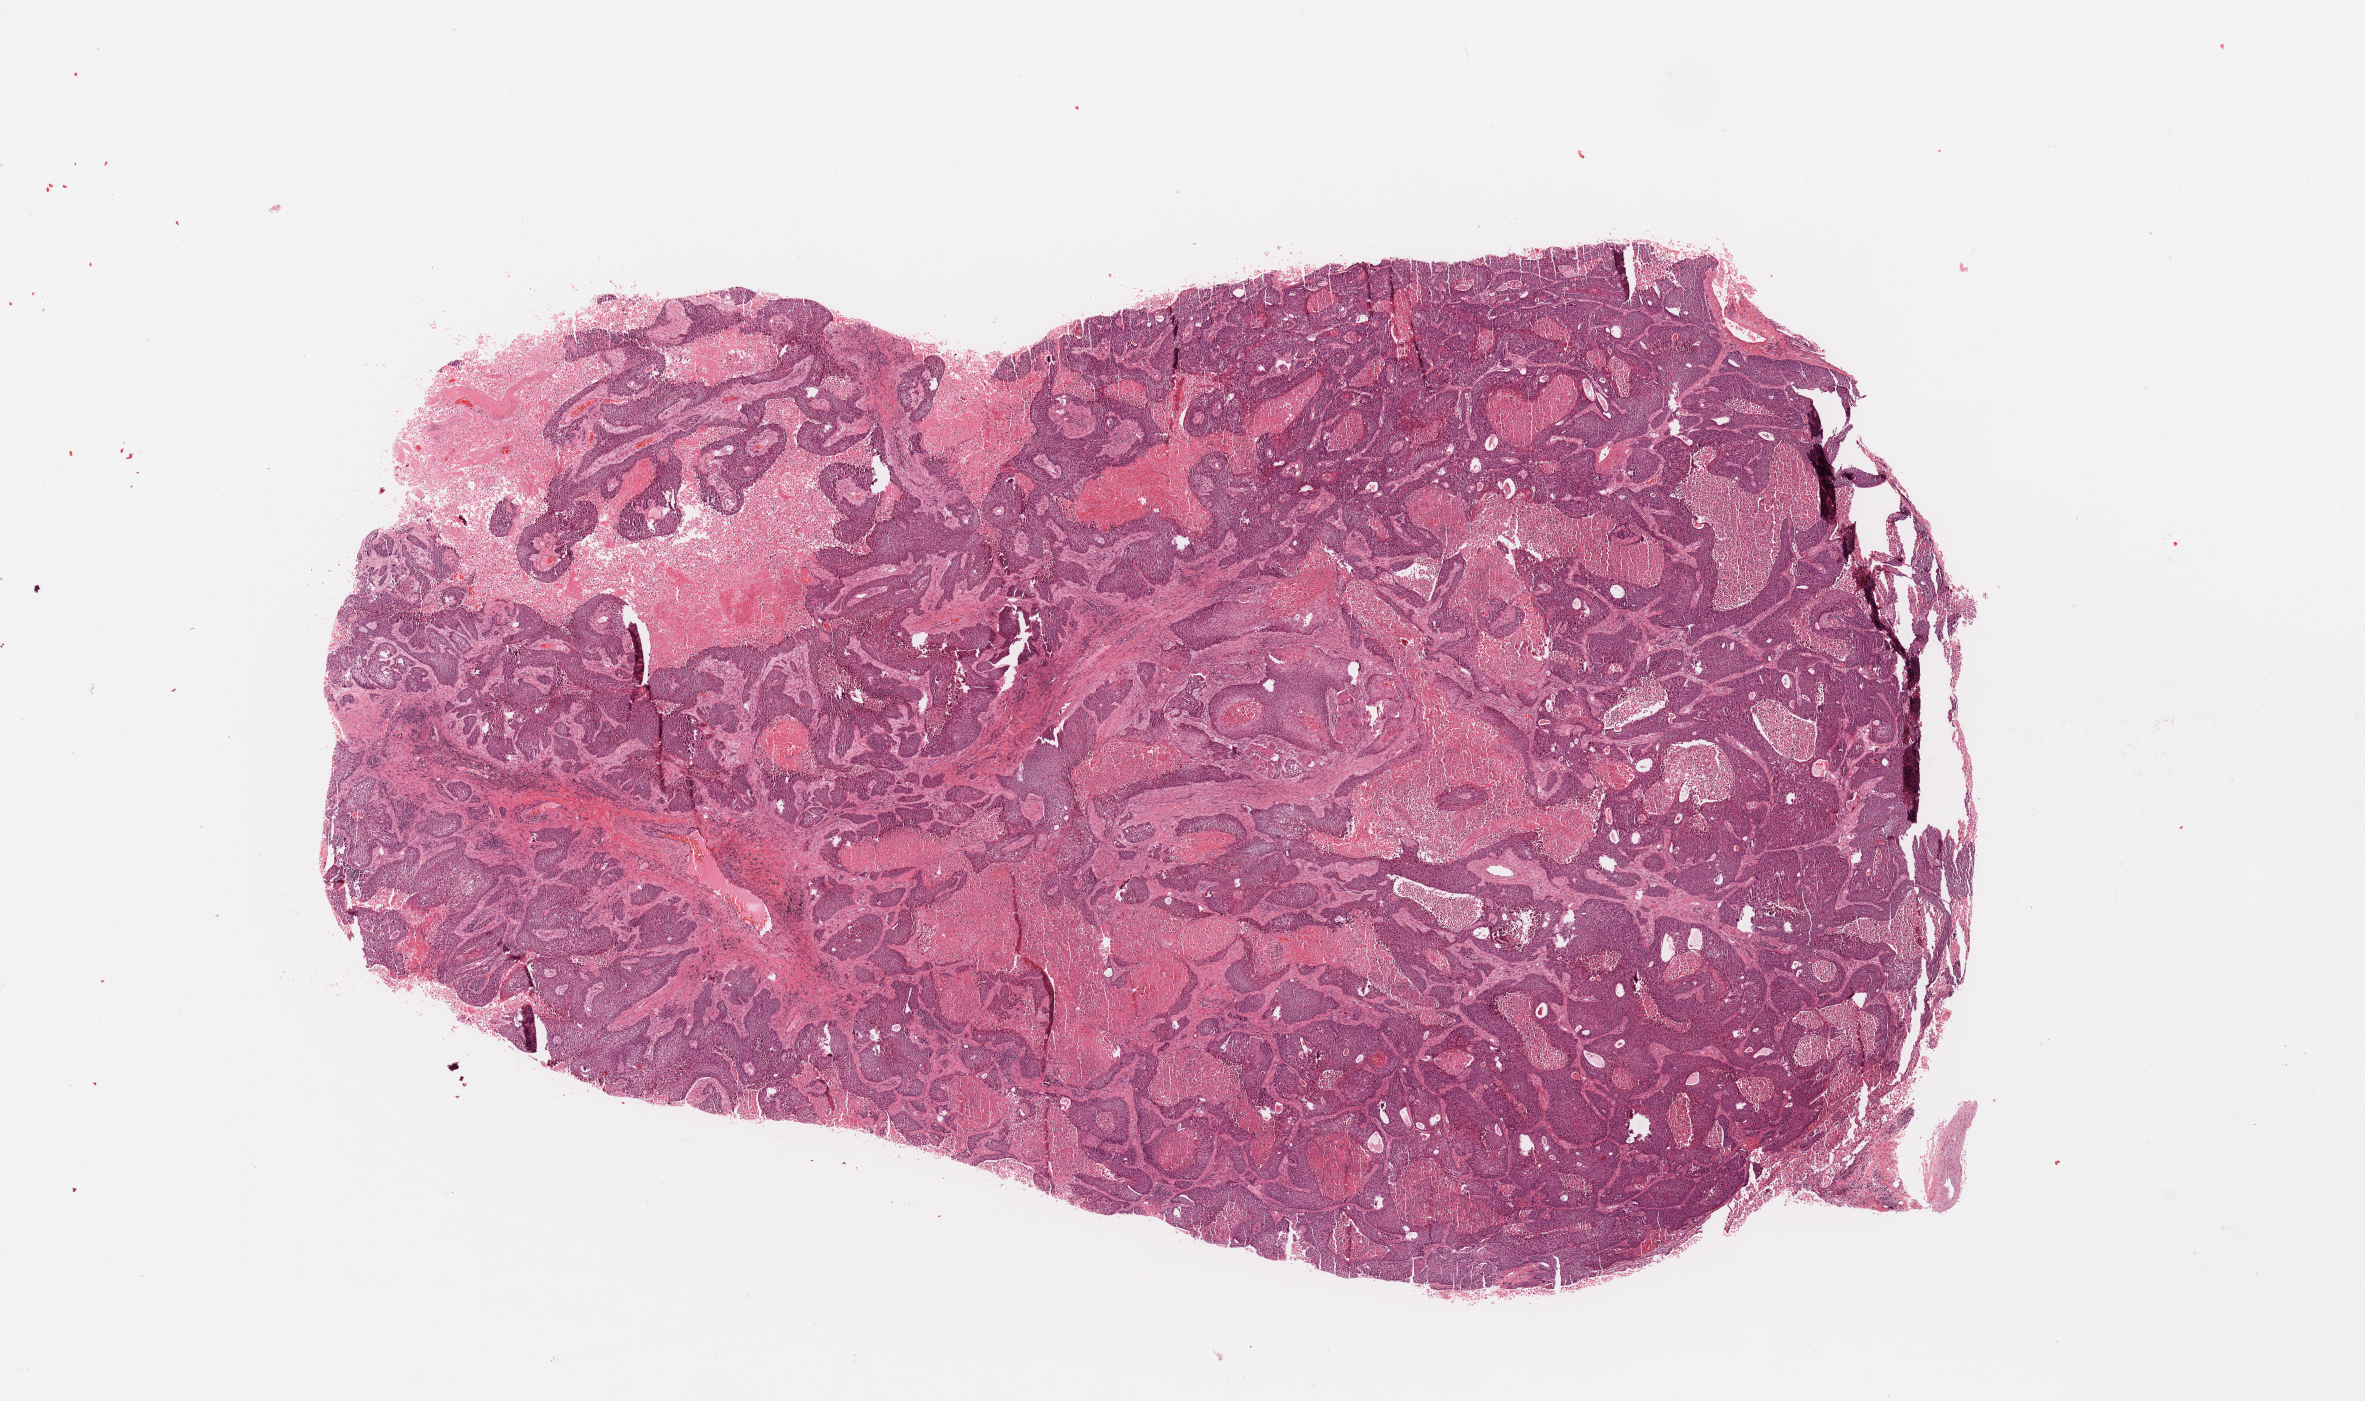
Whole-slide histology image, Hematoxylin and eosin (H&E) stained, a low-resolution overview of the entire scanned area, about 18.7 x 11.1 mm (from a 20x scan). Tumour tissue sample, sampled site: lung. 69-year-old male patient. Histologic grade: G2 (moderately differentiated). Composition of this section per pathologist review: tumour nuclei 65%, necrosis 15%.
AJCC pathologic stage: IA. Histologic diagnosis: Squamous cell carcinoma, NOS. Primary tumour site (as recorded): left lower lobe.